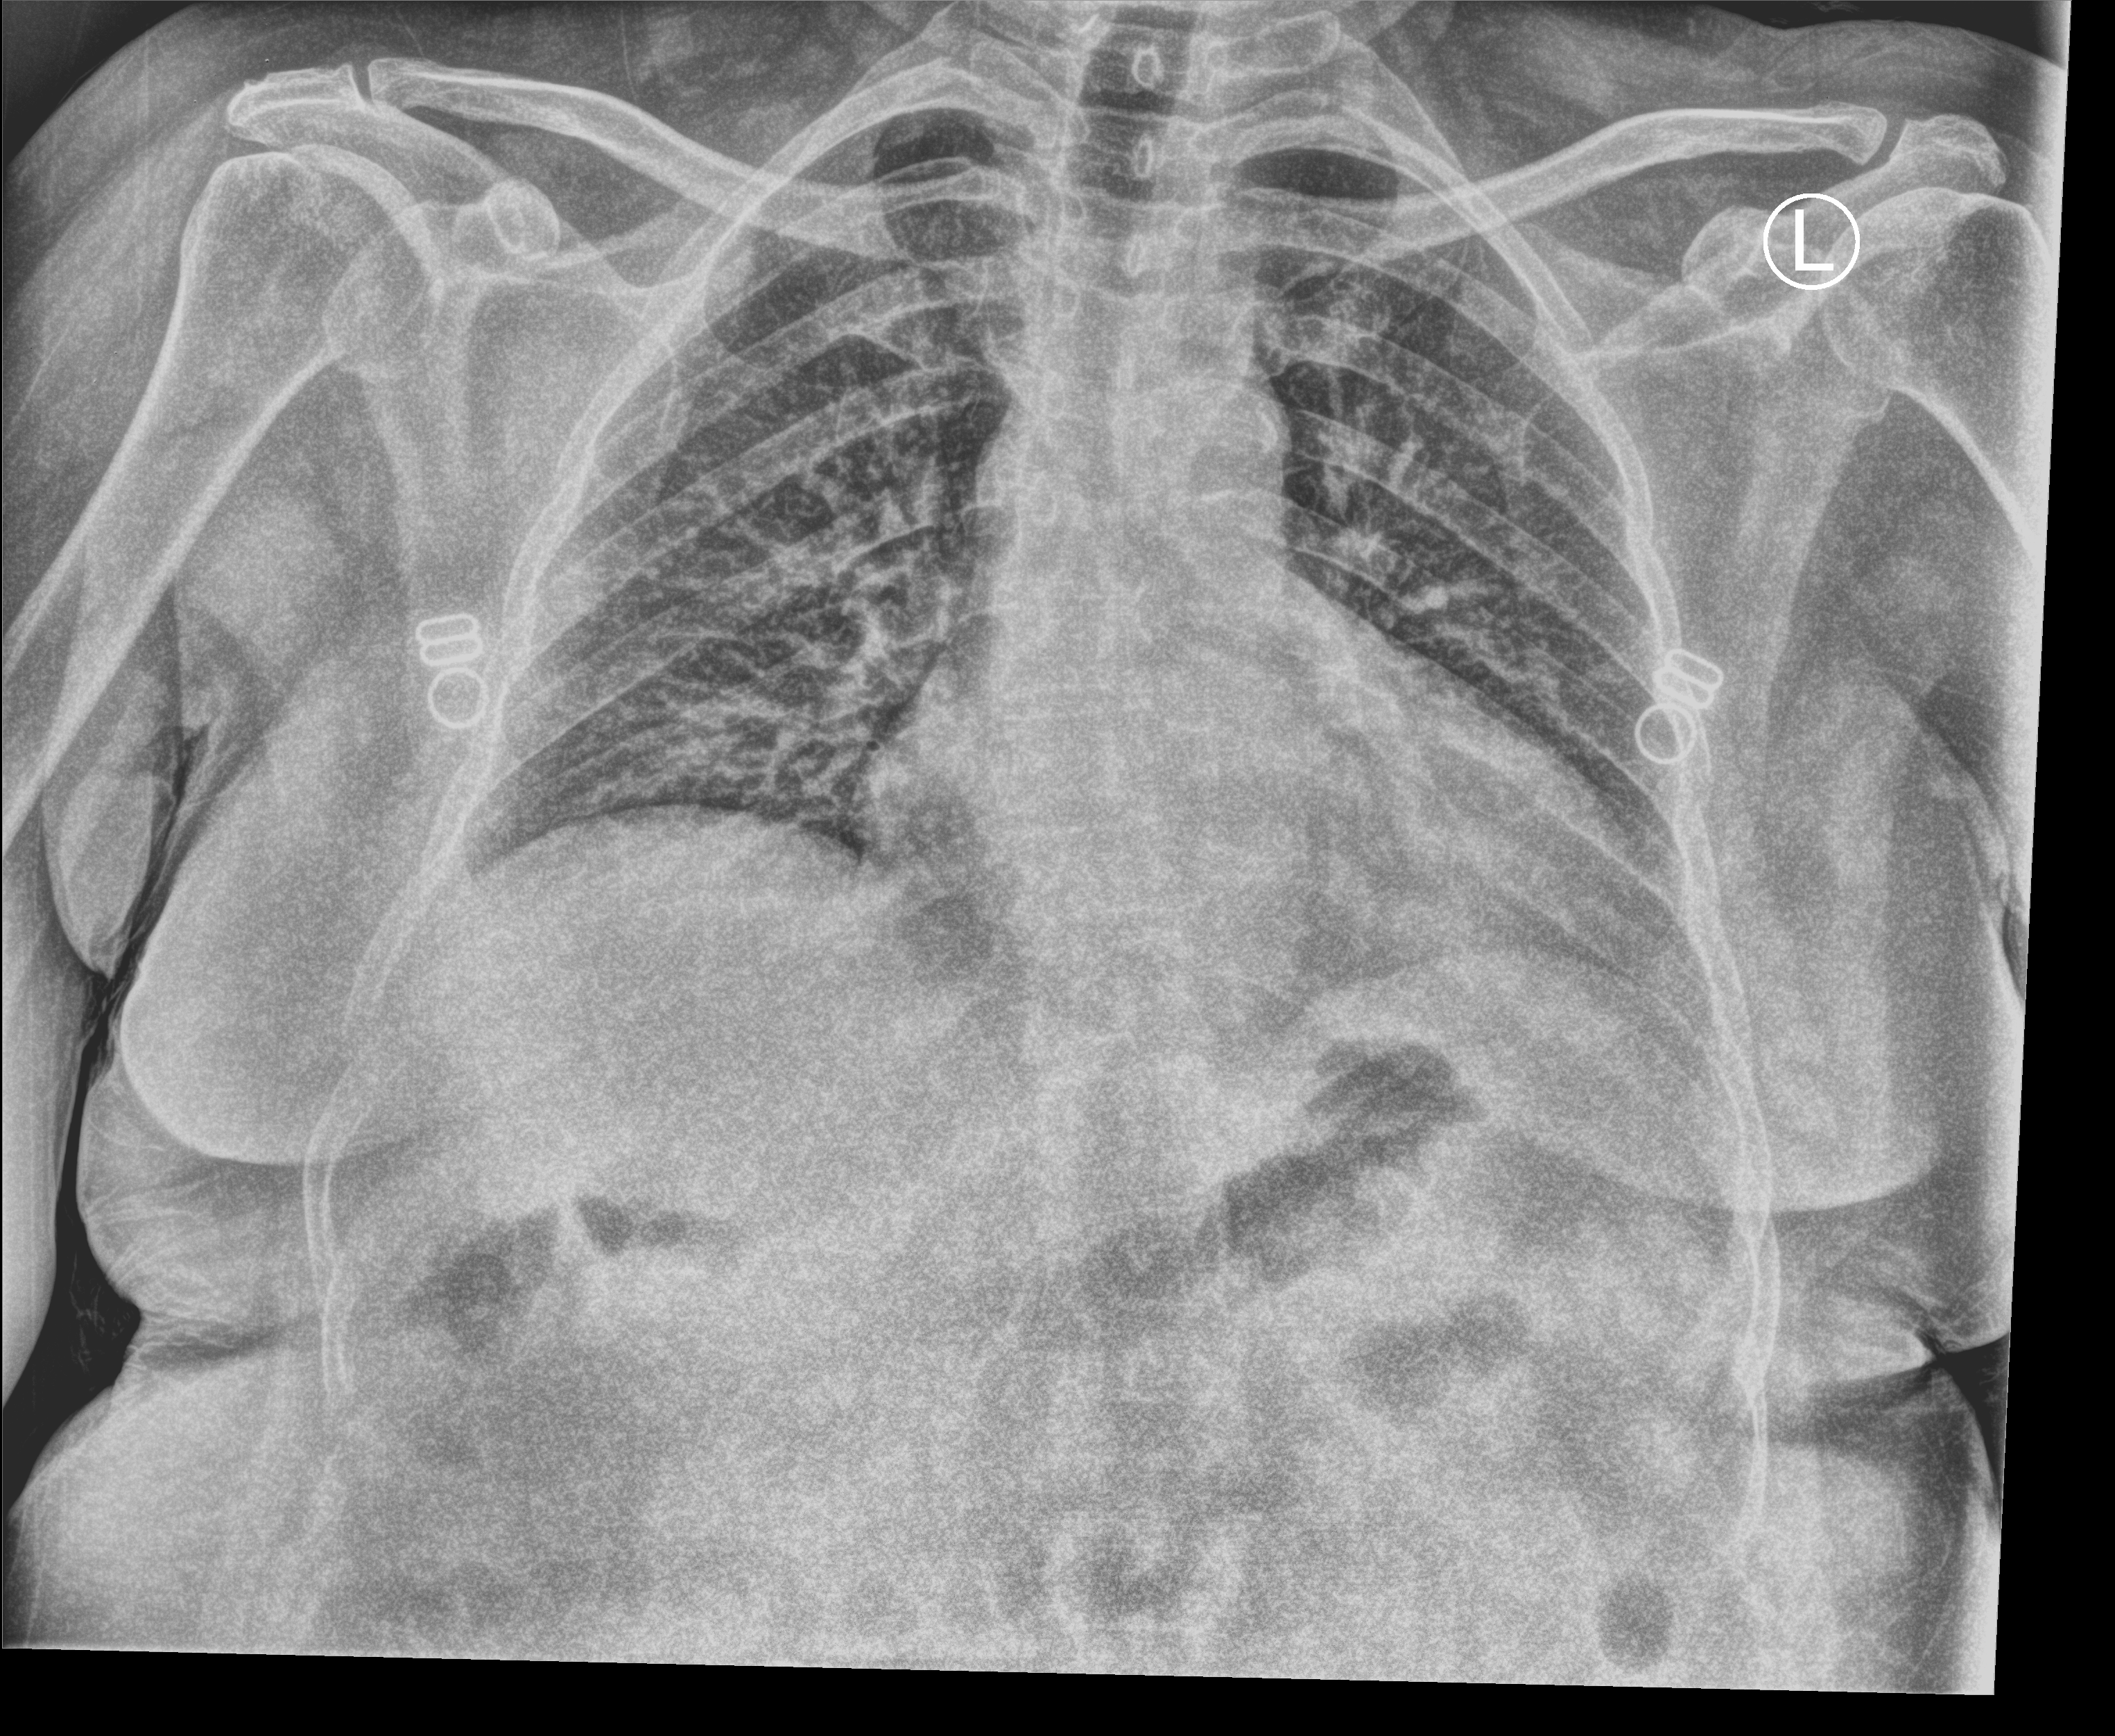
Bedside chest radiograph (computed radiography); anteroposterior (AP) projection. Patient hospitalised with COVID-19; female, aged 60–74 years.
From the hospital-stay record, not from the radiograph (when in the stay this image was taken is not recorded):
- admitted to intensive care during this hospital stay: no